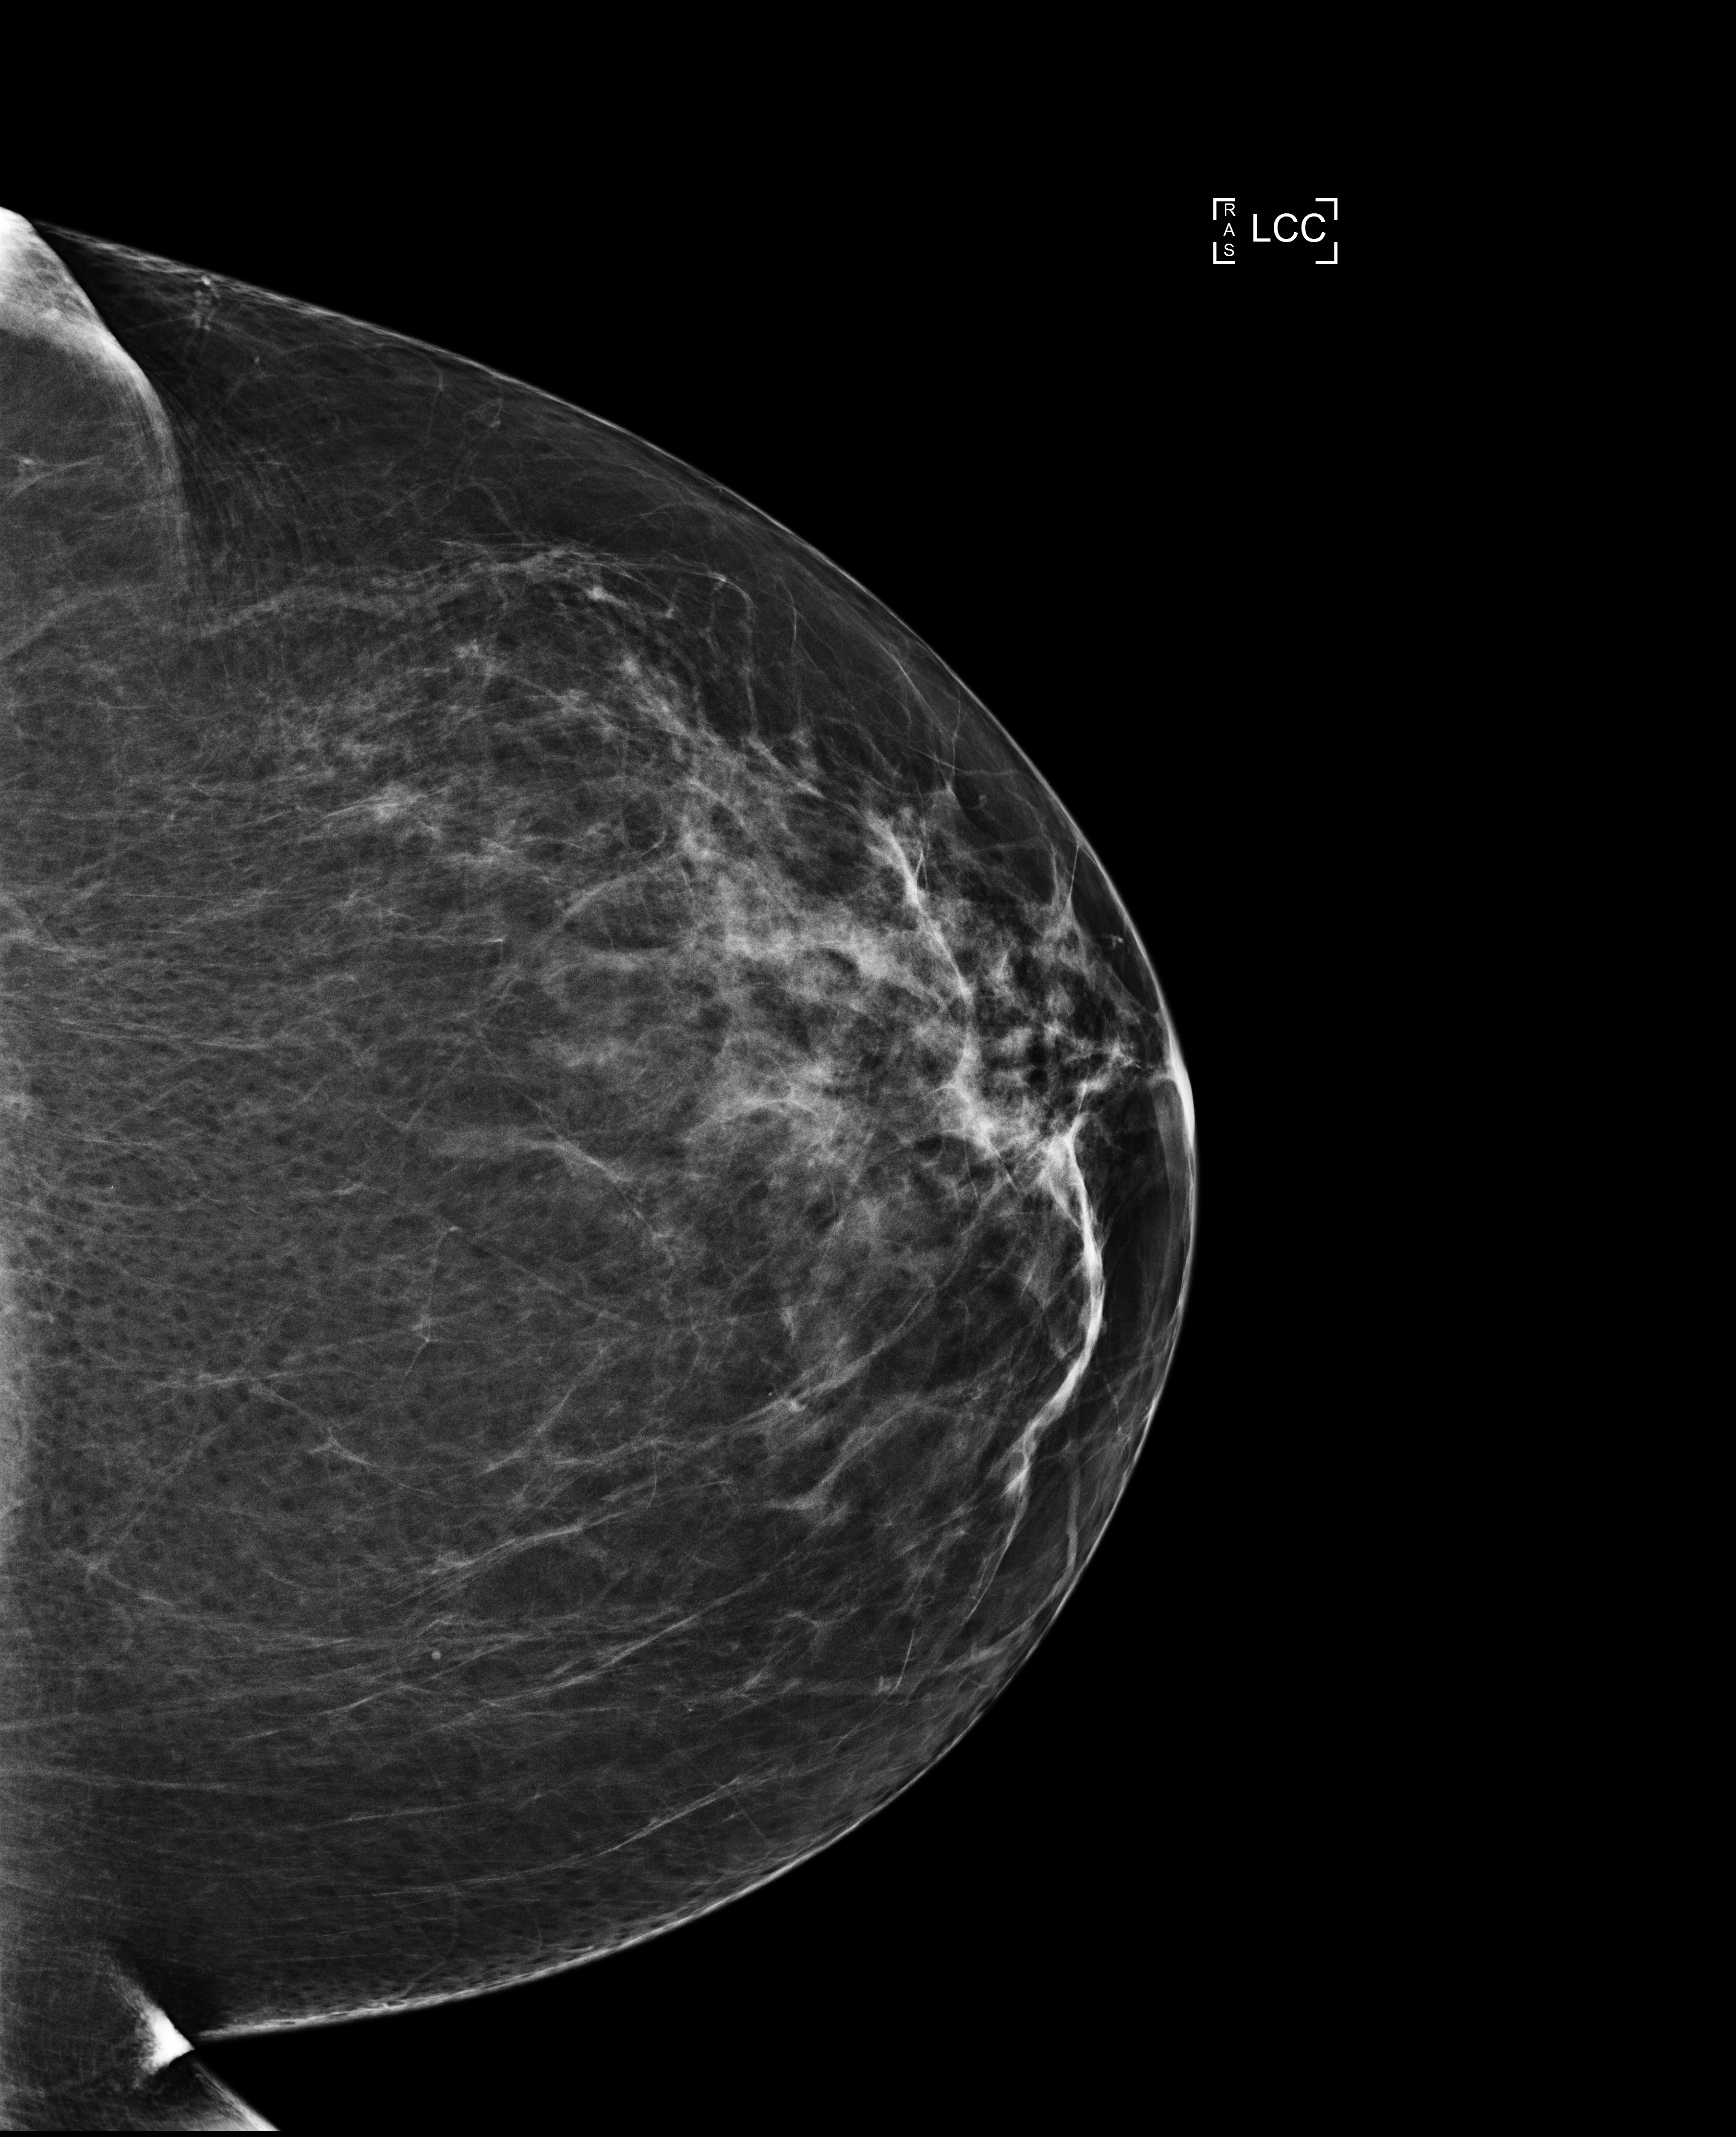
Digital mammogram (FFDM); left breast; craniocaudal (CC) view; annual screening mammography examination; system: Selenia Dimensions. Patient aged 66 years (female).
- breast density at the screening exam (both breasts): scattered fibroglandular densities (BI-RADS density category b)
- final BI-RADS assessment for this screening round (tomosynthesis exam, both breasts): category 1
- recall: no recall after this screen